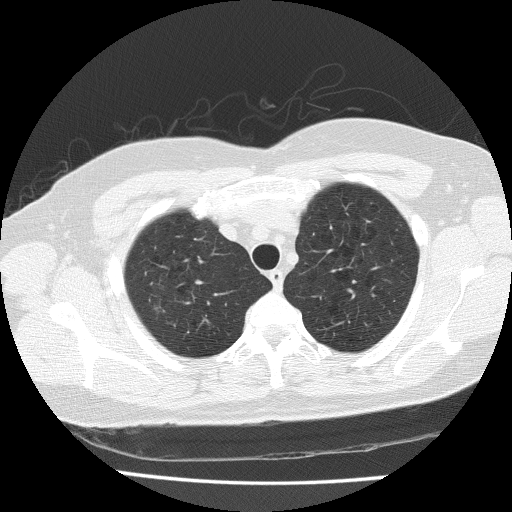
Chest CT (low-dose screening protocol), one axial image; baseline annual screen; lung window (W 1500 / L -600 HU); lung (sharp) reconstruction kernel (FC51); slice 28 of 175 in the series; 512 × 512 image matrix, field of view 340 × 340 mm. Female, age 57 years at enrolment.
Expert-annotated lung lesion, bounding box (x1, y1, x2, y2) in pixels: (140, 295, 180, 326). Reader record for this screening exam (exam-level; its link to the box is not recorded): non-calcified nodule or mass ≥4 mm, right upper lobe, 8 × 7 mm, spiculated (stellate) margins, soft tissue attenuation. Official screen result: positive, change unspecified: nodule(s) >= 4 mm or enlarging nodule(s), mass(es), or other non-specific abnormalities suspicious for lung cancer. Participant outcome: lung cancer diagnosed 132 days after this screen — bronchiolo-alveolar adenocarcinoma, NOS, right upper lobe, well differentiated (G1), stage IA (AJCC 6th edition), 12 mm at pathology.